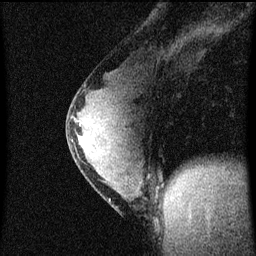
Breast MRI (dynamic contrast-enhanced), one sagittal slice; slice 31 of 60 in the series (ordered by position); dynamic contrast-enhanced series, image 2 of 4 at this slice position (ordered by acquisition); 1.5 T; TE 4.2 ms, TR 8 ms; 2 mm slice thickness; 256 × 256 image matrix. Female patient, age 33 years.
Outlined on this slice (semi-automatic segmentation, software-assisted and operator-edited):
- analysis volume of interest (the breast-tissue region the enhancement analysis was run in; not a lesion): bounding box (x1, y1, x2, y2) in pixels: (67, 76, 155, 217)
- tumour enhancement mask (voxels above the 70 % enhancement threshold inside the analysis volume of interest): (72, 110, 99, 173)